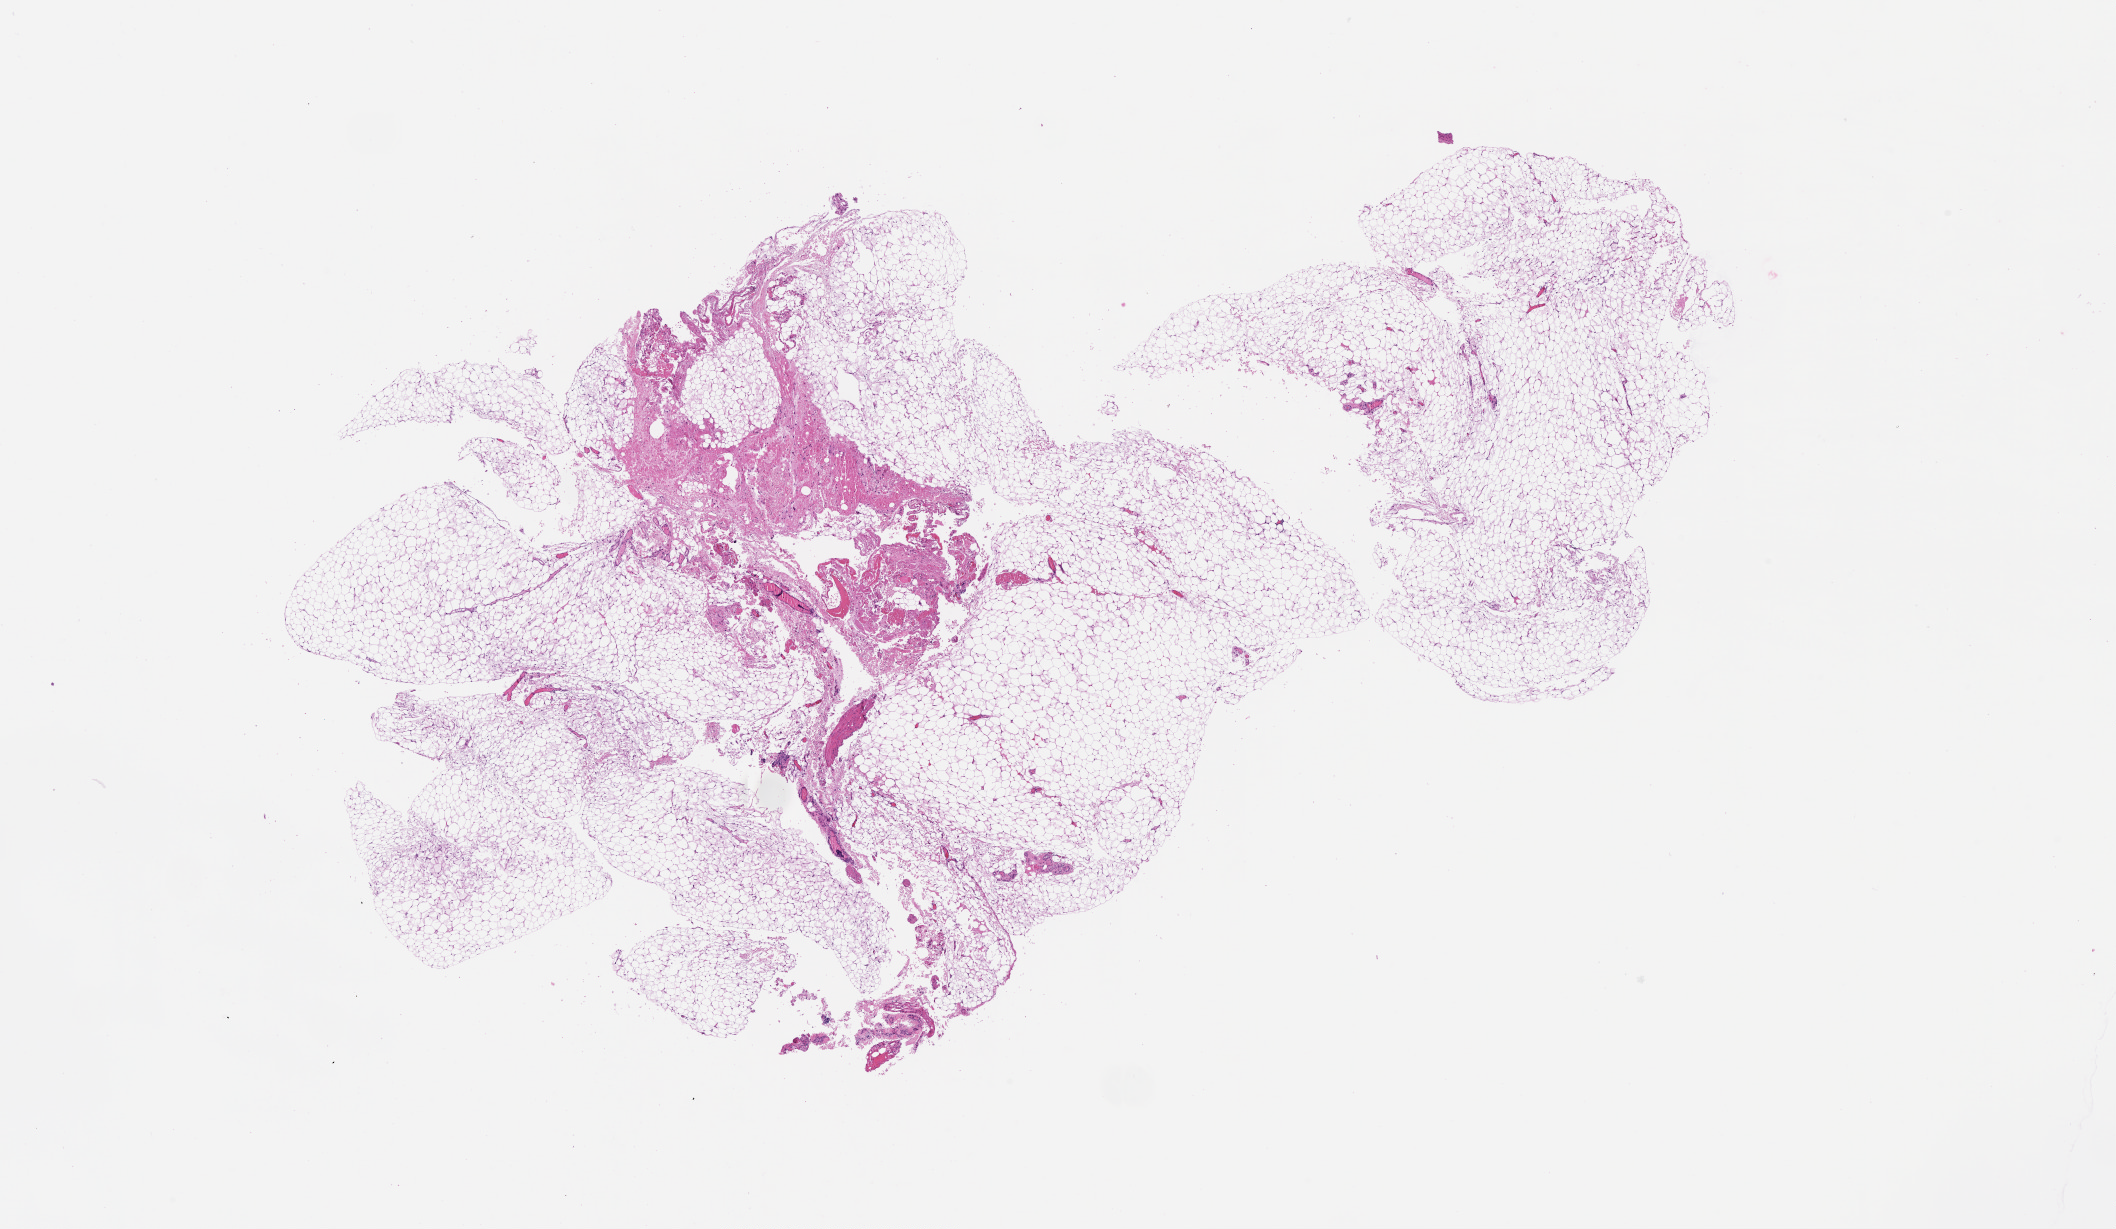
Digitized H&E-stained tissue section (whole slide), whole scanned area (about 17.0 x 9.9 mm, from a 20x scan) shown as a low-resolution overview.
Patient diagnosis (cohort enrolment): sarcoma (site not recorded at cohort level).